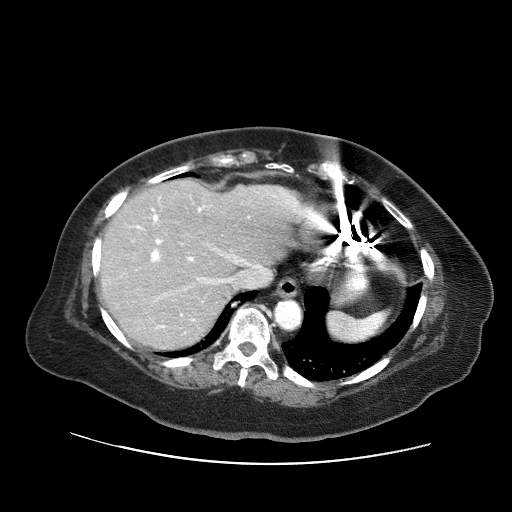
Contrast-enhanced abdominal CT (liver protocol), one axial slice. Slice 49 of 71 in the series (ordered by position). Soft-tissue window (W 400 / L 40 HU). 512 × 512 image matrix, field of view 400 × 400 mm. From the clinical record (not read from this slice): diagnosis: hepatocellular carcinoma (patient treated with transarterial chemoembolisation; whether this scan precedes or follows treatment is not stated here); TNM stage (as recorded): Stage-II; Child-Pugh class: A; tumour nodularity: multinodular; tumour size: 5 cm.
Annotated regions visible in this slice (semi-automatically segmented with operator editing):
- liver parenchyma outside the tumour (the mass and vessels are separate outlines, so this box may not span the whole liver): bounding box <99,178,302,350> (left, top, right, bottom; pixels)
- liver vessels: <131,190,299,329>